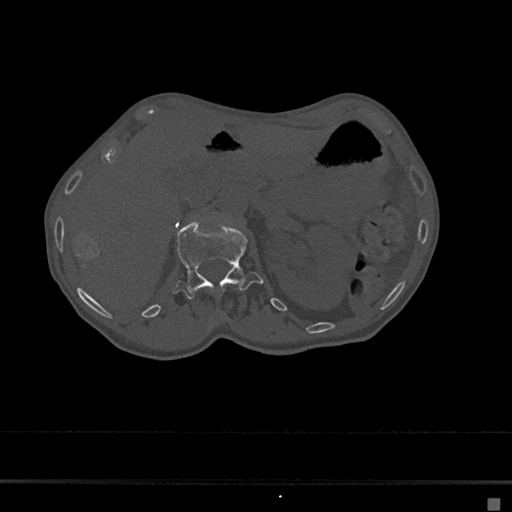
CT including the spine, one axial slice. Position 74 of 797 along the scan axis. Reconstruction kernel Br40s/3. Bone window (W 1800 / L 400 HU). 0.5 mm slice thickness. 512 × 512 image matrix, field of view 360 × 360 mm. Patient: female, 68 years. Case-level facts recorded for this patient, not image findings: primary cancer: renal.
Structures marked on this image (semi-automatic segmentation, software-assisted and operator-edited):
- L1 vertebra: box from (x=173, y=219) to (x=263, y=299) px
- T12 vertebra: (x=215, y=317)–(x=220, y=323)